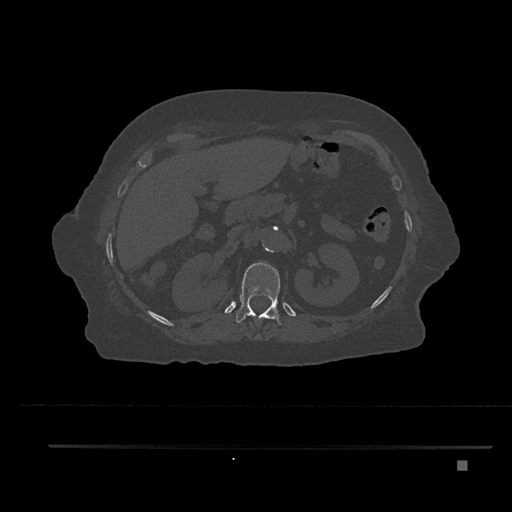
CT including the spine, one axial slice; position 265 of 797 along the scan axis; reconstruction kernel Br40s/3; bone window (W 1800 / L 400 HU); 512 × 512 image matrix, field of view 437 × 437 mm. Patient: female, 76 years. From the clinical record (not read from this slice): primary cancer: lung; vertebrae with lytic lesions (as recorded): T11, L3.
Outlined on this slice (semi-automatic segmentation, software-assisted and operator-edited):
- T12 vertebra: box from (x=236, y=262) to (x=282, y=337) px